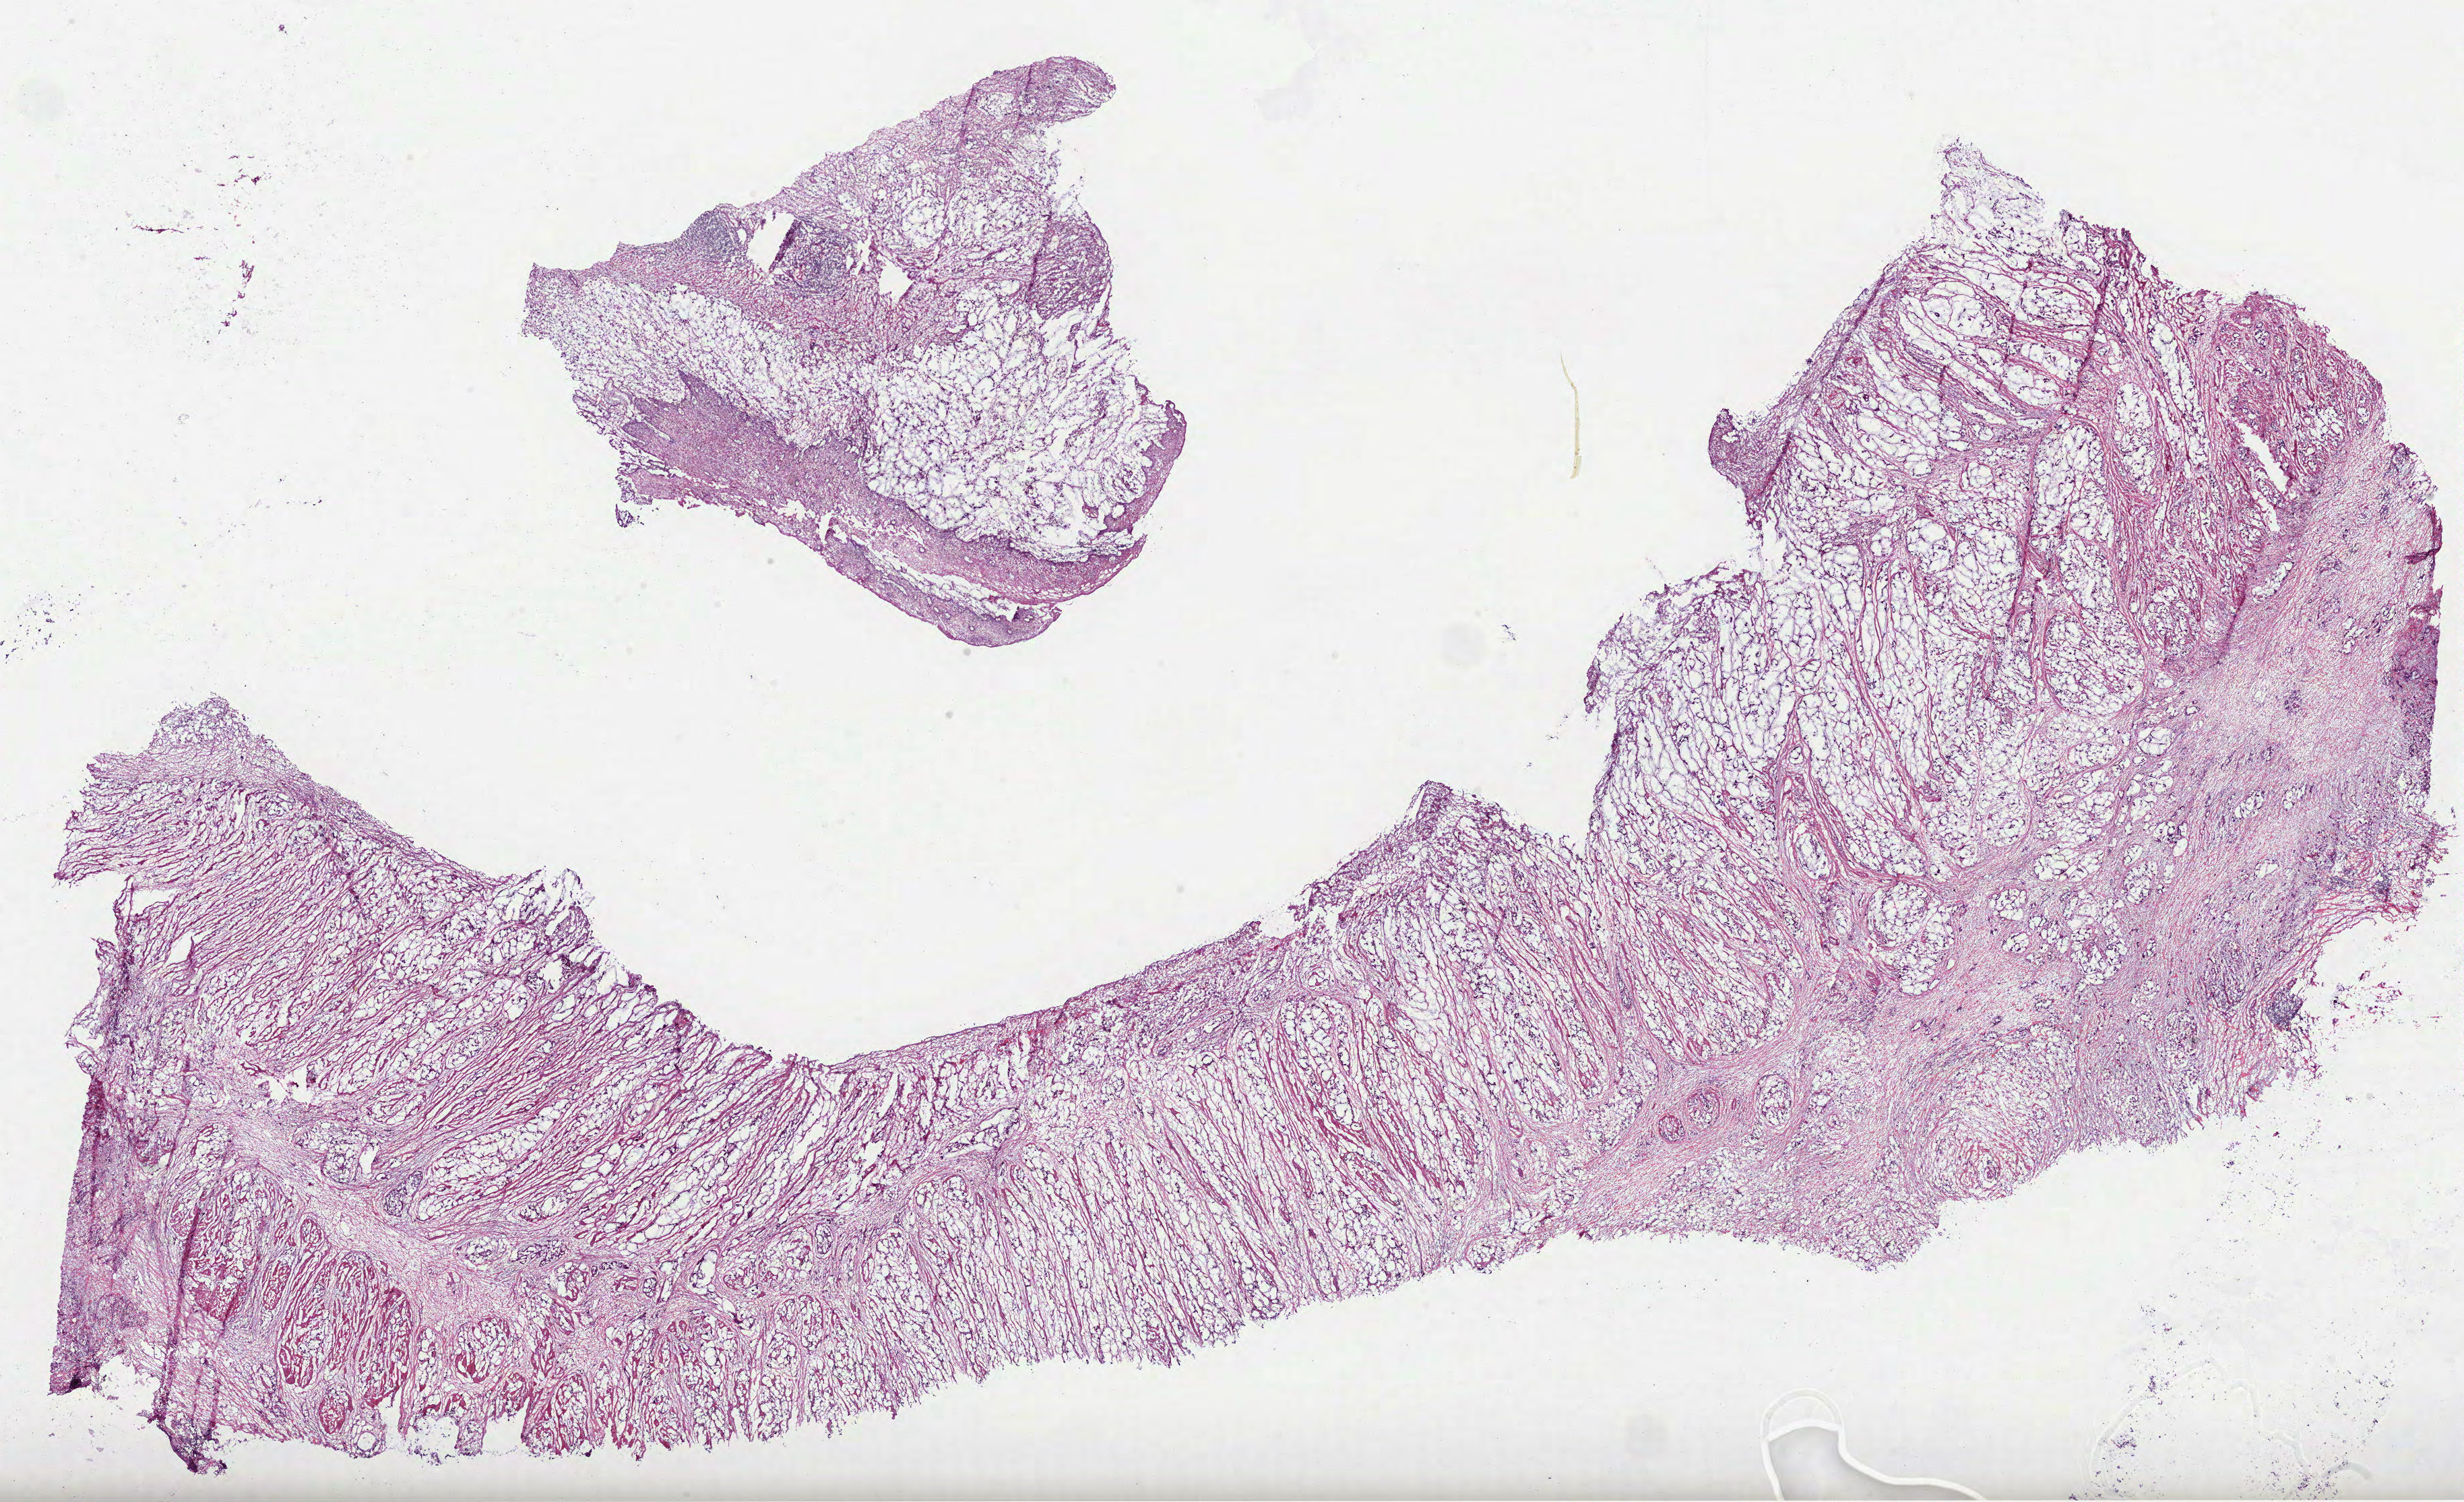
Digitized H&E tissue section (whole slide) — shown as a low-resolution overview of the whole scanned area (about 29.5 x 18.0 mm, from a 40x scan); frozen section from the top of the tissue portion; sample: primary tumour, stomach. Patient: male, age at initial diagnosis 59 years. Histologic grade: G3 (poorly differentiated). Slide review estimates, as recorded: tumour cells 65%, tumour nuclei 70%, normal cells 5%, stromal cells 30%, necrosis 0%.
Pathologic diagnosis: Mucinous adenocarcinoma (cardia, NOS). AJCC pathologic stage: IIIA.